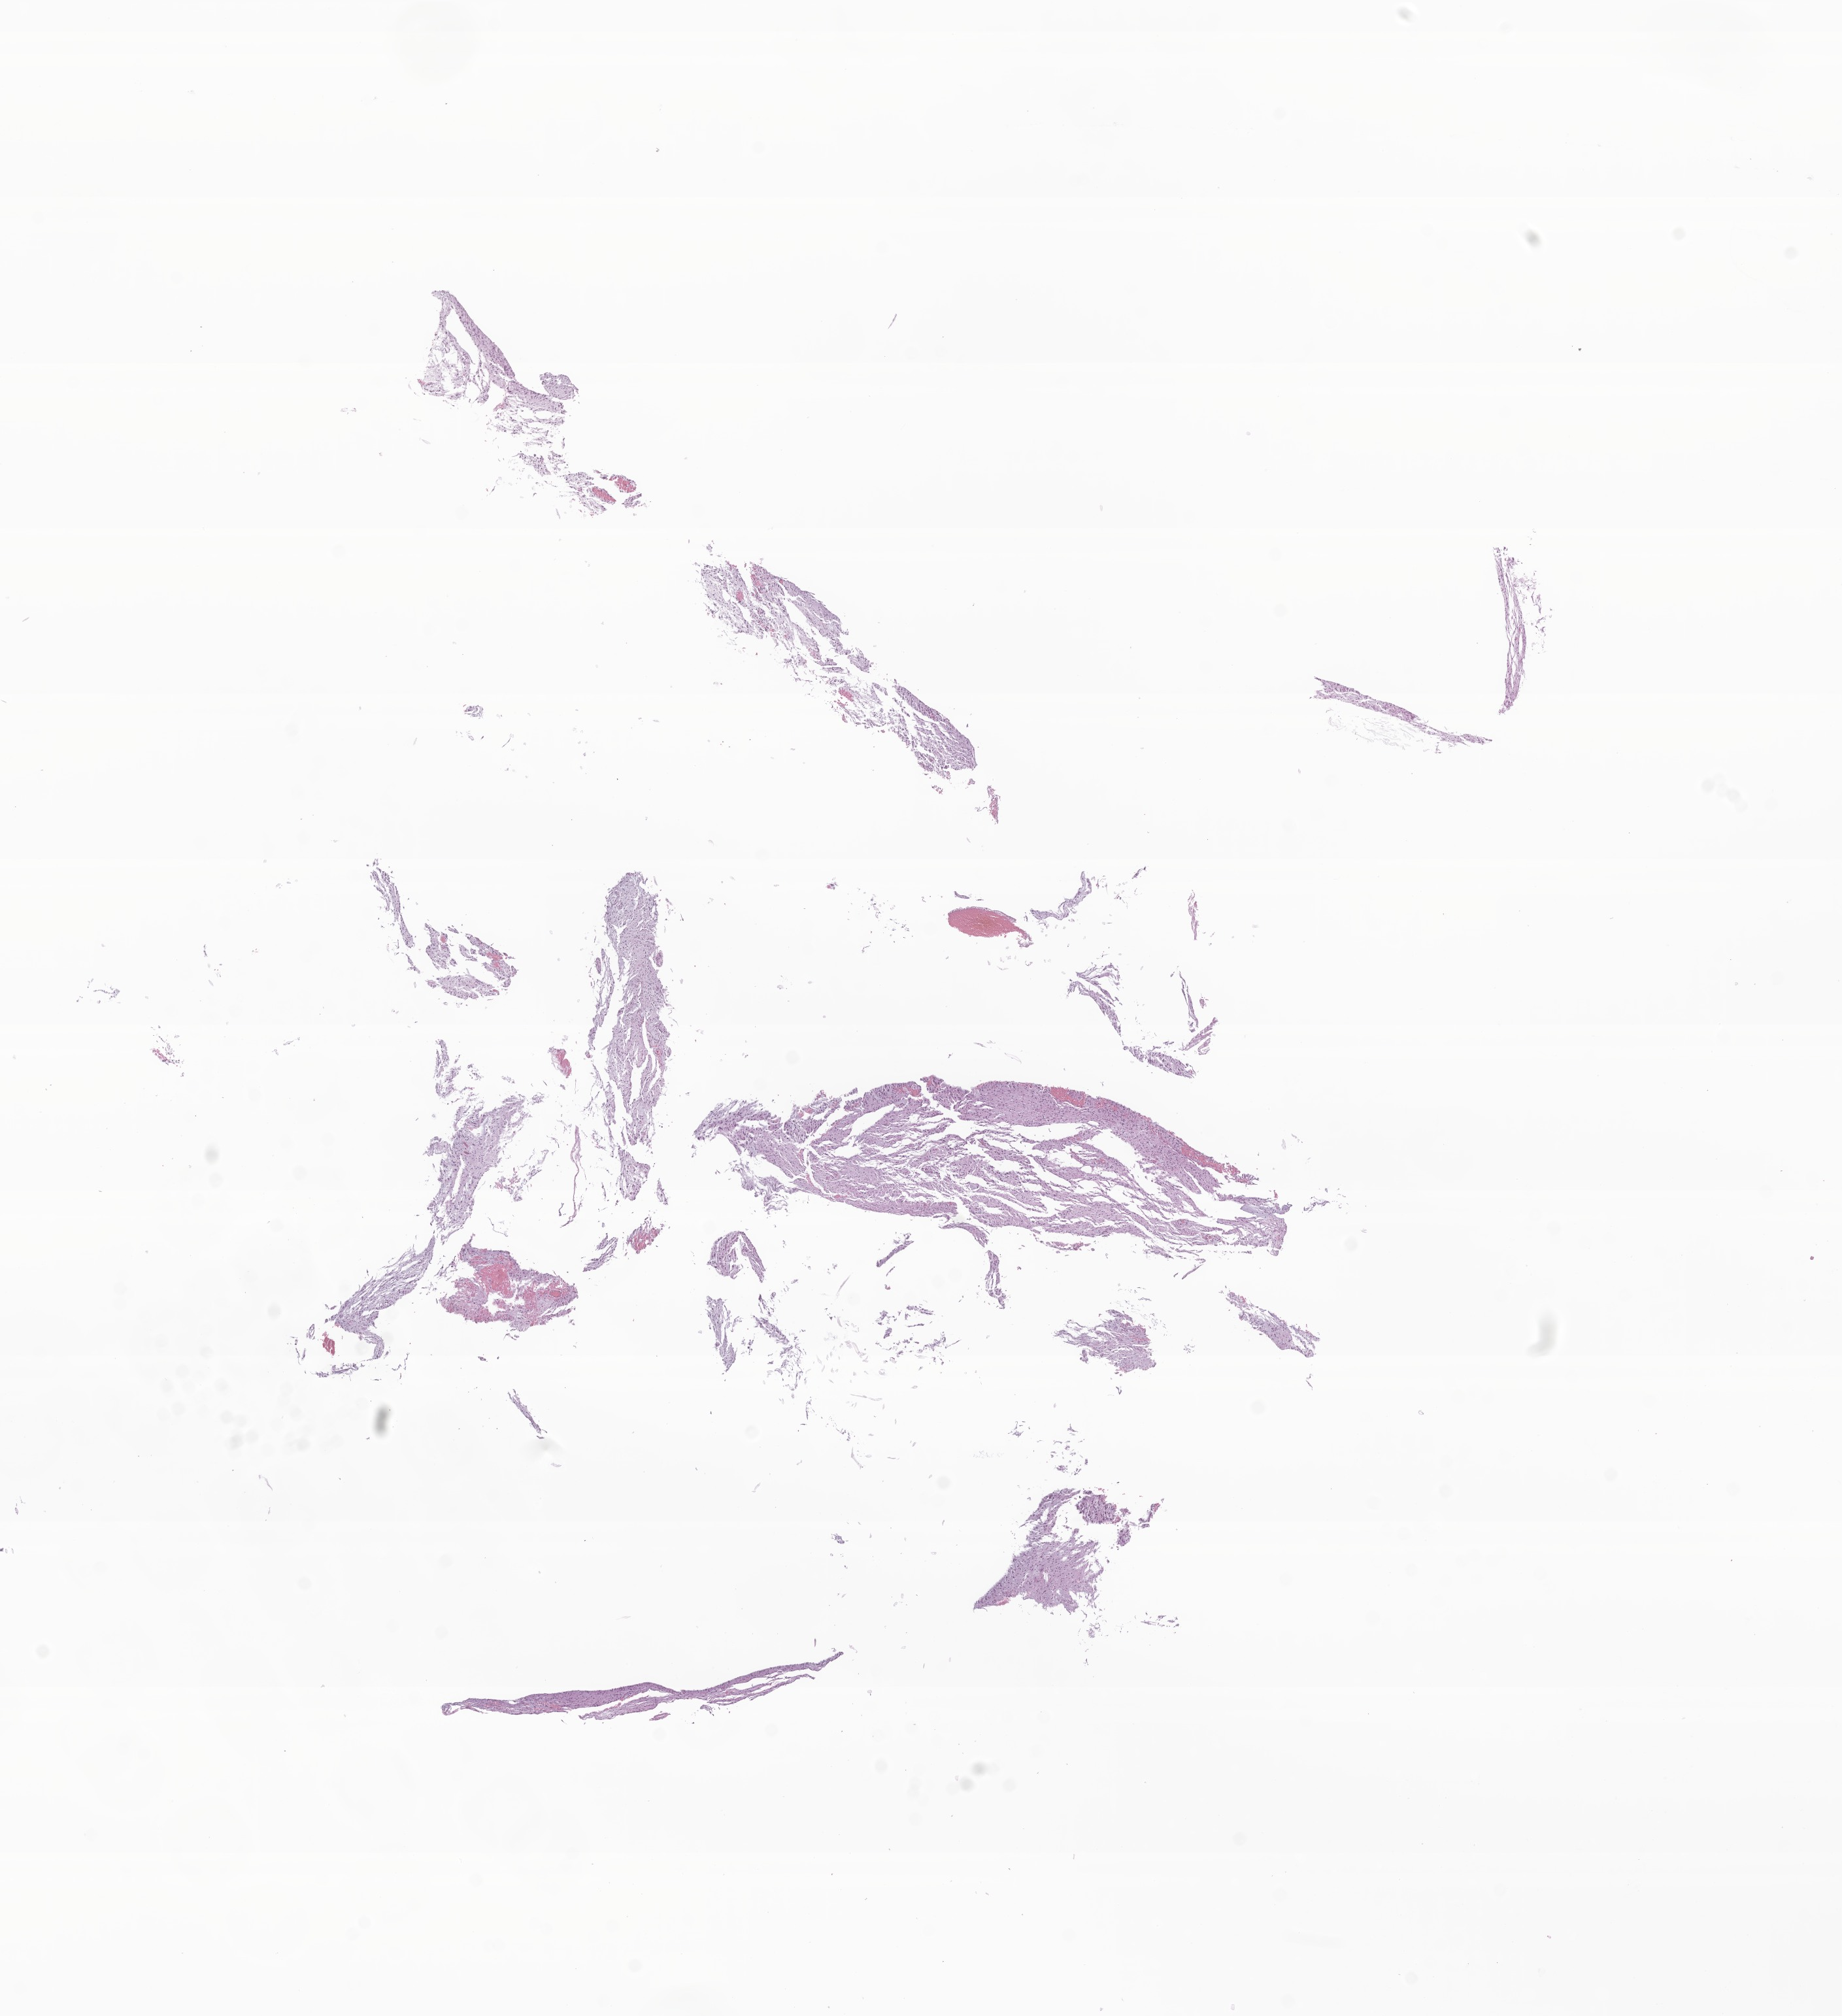
Digitized haematoxylin and eosin-stained section of tumor tissue from the brain, a low-resolution overview of the entire scanned area, about 11.9 x 13.0 mm; formalin-fixed, paraffin-embedded (FFPE) tissue. Patient male; age 187 months (15 years 7 months).
Recorded diagnosis: Pilocytic astrocytoma.